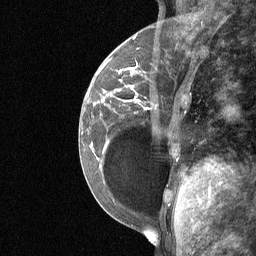
Breast MRI (dynamic contrast-enhanced), one sagittal slice. Position 20 of 64 along the scan axis. Dynamic contrast-enhanced study with each time point stored as its own series, time point 2 of 3 at this slice position (early post-contrast, ordered by acquisition time). 1.5 T. TE 4.8 ms, TR 27 ms. 256 × 256 image matrix, field of view 200 × 200 mm. Patient: female, 34 years. Case-level facts recorded for this patient, not image findings: setting: breast cancer imaged before/during neoadjuvant chemotherapy; receptor status: HR-positive, HER2-negative.
Structures marked on this image (semi-automatically segmented with operator editing):
- analysis volume of interest (the breast-tissue region the enhancement analysis was run in; not a lesion): bounding box (x1, y1, x2, y2) in pixels: (92, 50, 188, 185)
- tumour enhancement mask (voxels above the 90 % enhancement threshold inside the analysis volume of interest): (119, 68, 148, 109)